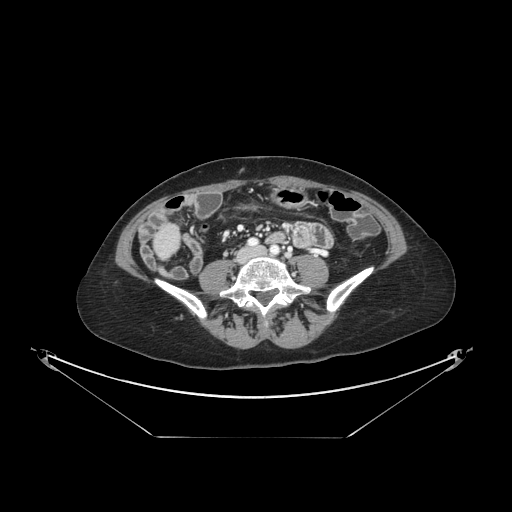
Contrast-enhanced abdominal CT, one axial slice. Position 18 of 148 along the scan axis. 120 kVp. Intravenous contrast given. Soft-tissue window (W 400 / L 40 HU). 2.5 mm slice thickness. 512 × 512 image matrix, field of view 500 × 500 mm. Female patient, age 73 years. Case-level facts recorded for this patient, not image findings: diagnosis: colorectal cancer liver metastases, imaged before liver resection; multiple liver metastases: no; largest metastasis: 1 cm; chemotherapy before resection: yes.
Annotated regions visible in this slice (outlined manually by an expert reader):
- liver: box from (x=156, y=229) to (x=178, y=257) px